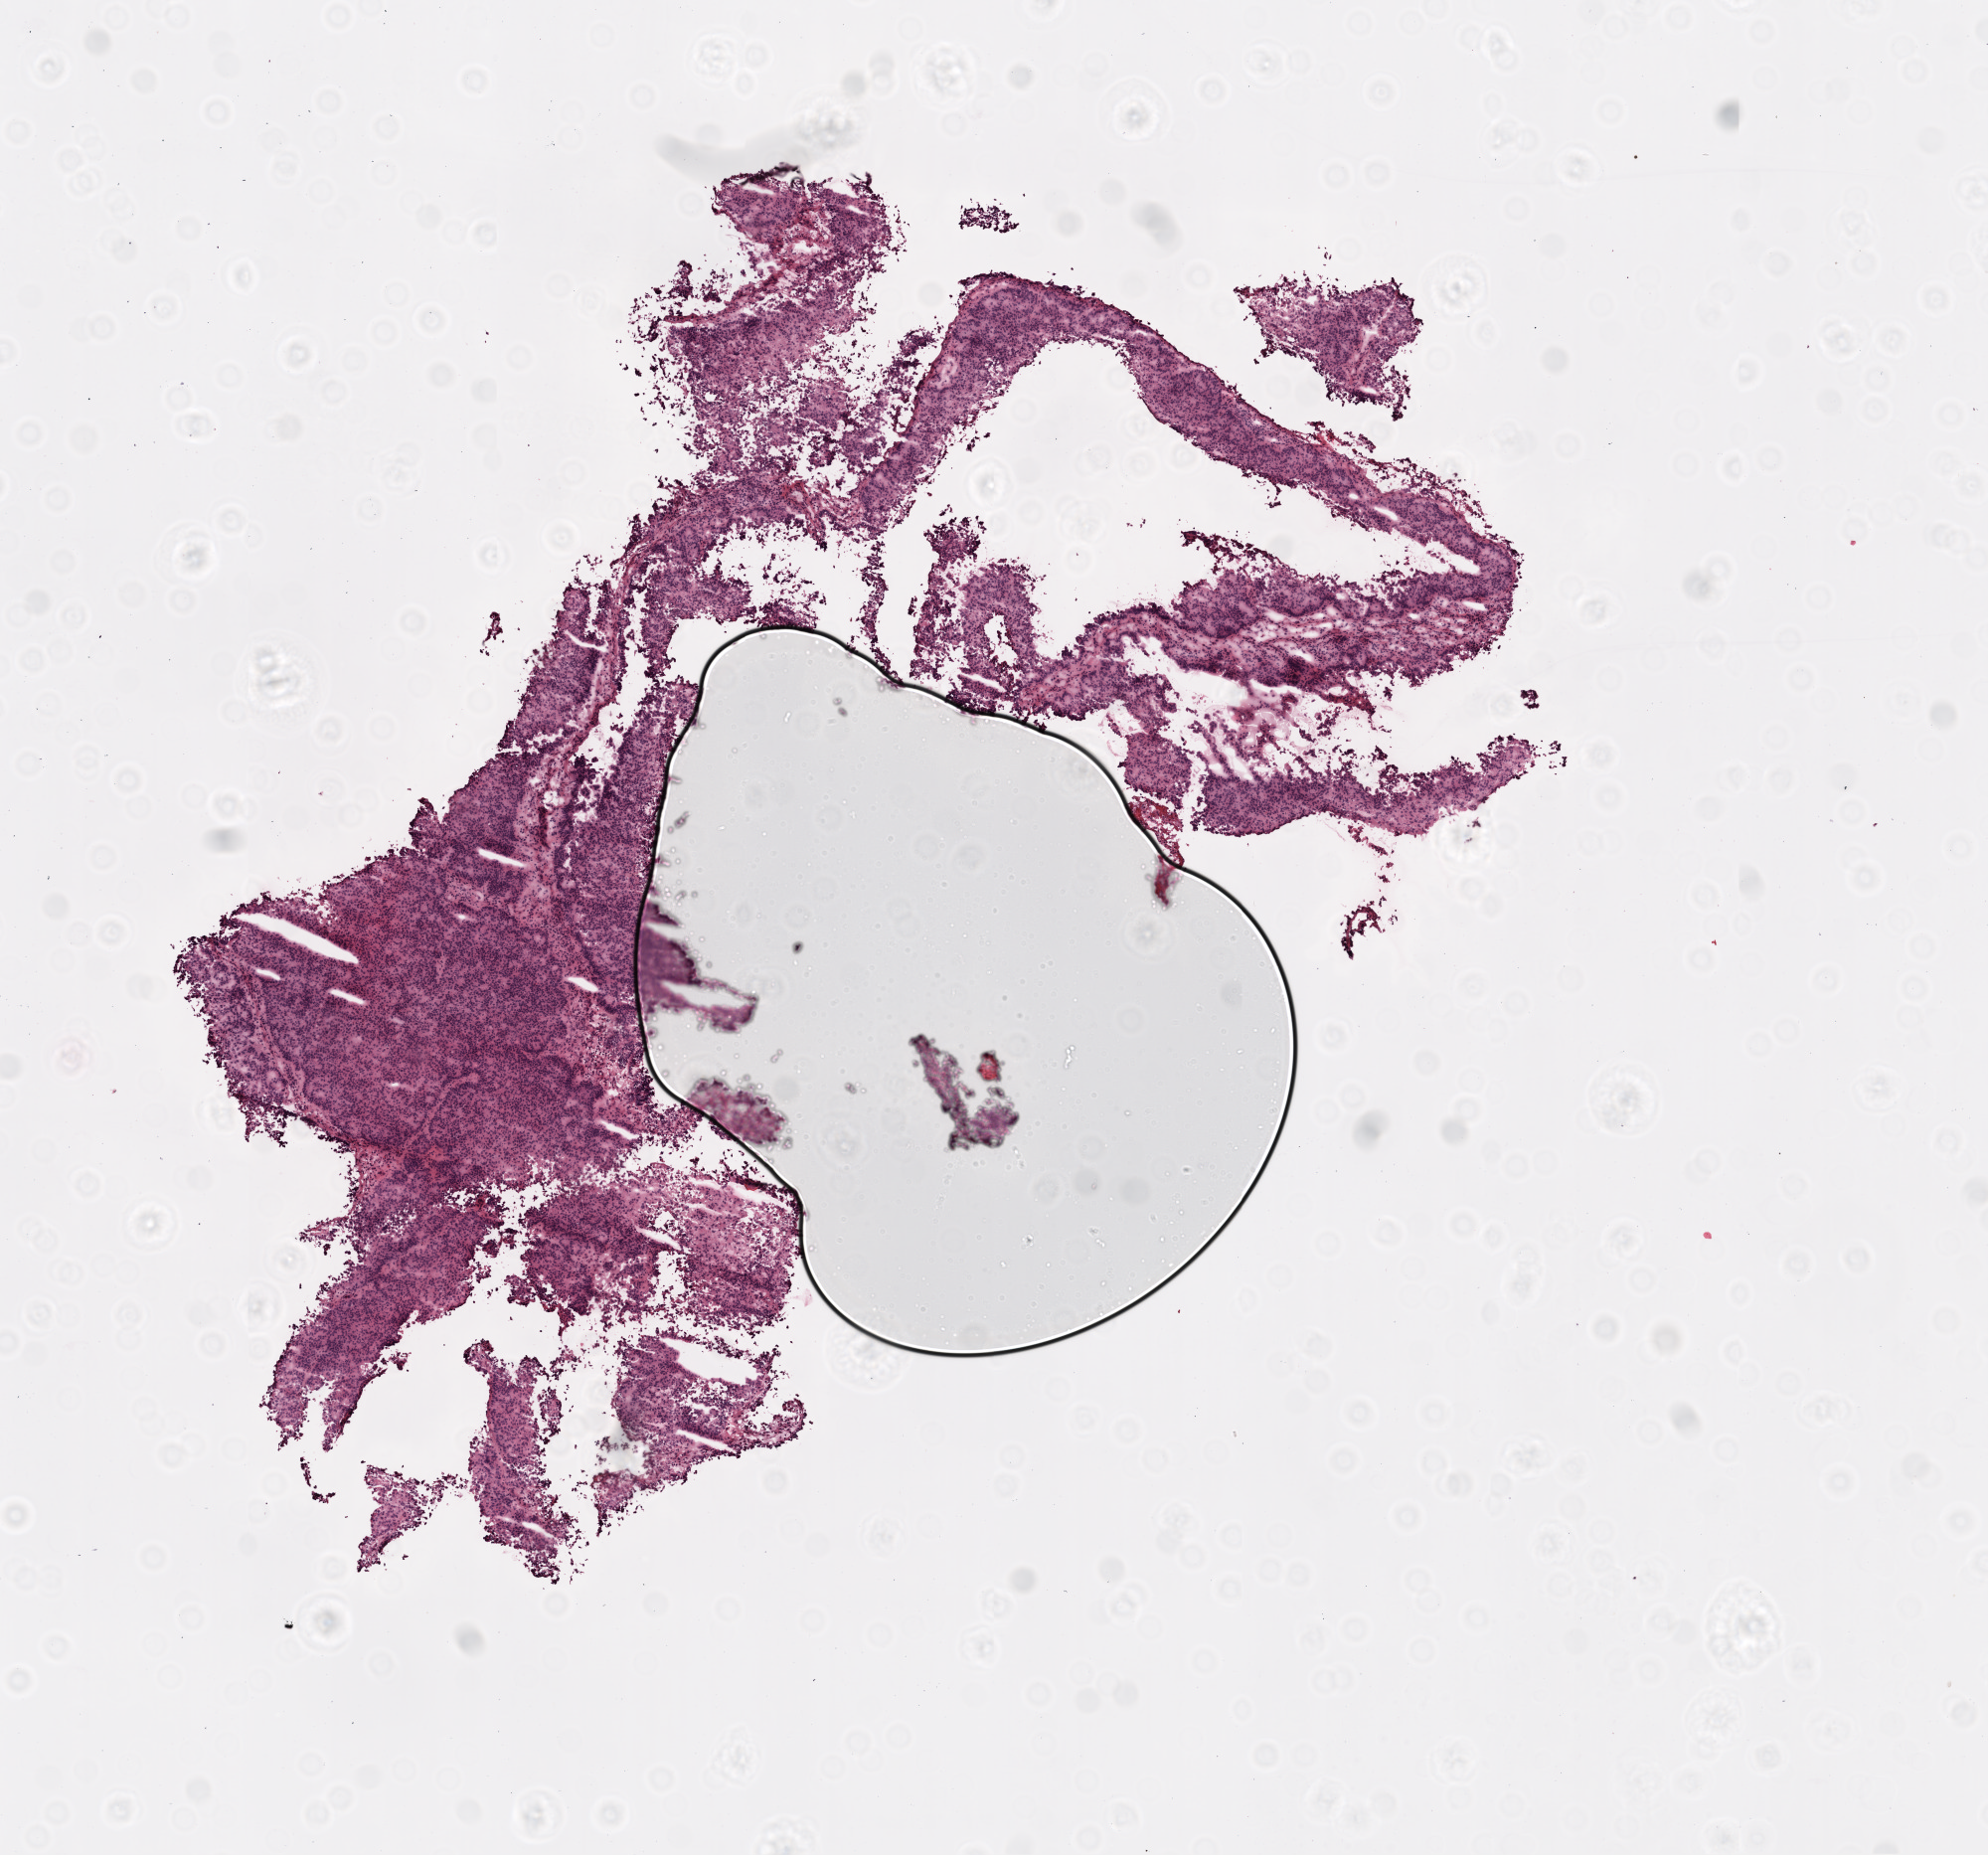
Whole-slide histology image, H&E — a low-resolution overview of the entire scanned area, about 8.0 x 7.5 mm (slide scanned at 20x). Frozen section from the top of the tissue portion. Ovary, recurrent tumour sample. Patient: female, age at initial diagnosis 61 years. Pathologist review of this section (percent, as recorded): tumour cells 90%, tumour nuclei 90%, normal cells 0%, stromal cells 10%, necrosis 0%.
This section: recurrent tumour. Patient diagnosis: Serous cystadenocarcinoma, NOS.